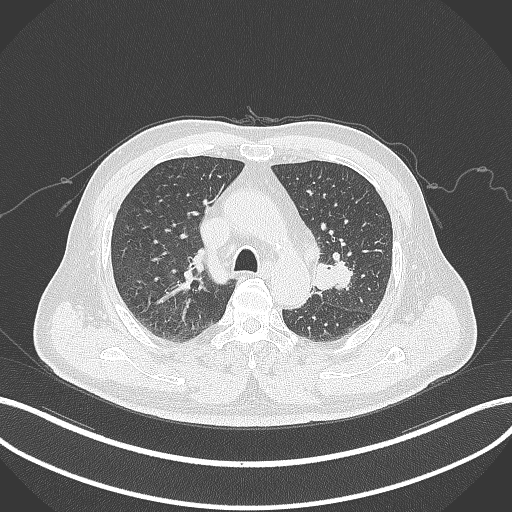
Chest CT, one axial slice. Position 207 of 286 along the scan axis. Reconstruction kernel B70f. 120 kVp. Lung window (W 1500 / L -600 HU). 1 mm slice thickness. 512 × 512 image matrix, field of view 400 × 400 mm. Male patient, age 67 years. Case-level facts recorded for this patient, not image findings: clinical TNM (as recorded): T2a N1 M0; histopathological grade: G3.
Structures marked on this image (rectangle marked by the reading radiologist):
- lung tumour (recorded histology: adenocarcinoma): bounding box (x1, y1, x2, y2) in pixels: (310, 259, 357, 293)